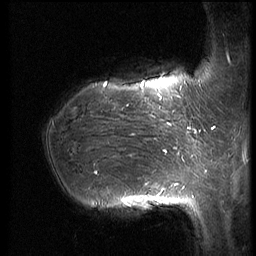
Breast MRI (dynamic contrast-enhanced), one sagittal slice; position 19 of 66 along the scan axis; dynamic contrast-enhanced series, image 2 of 3 at this slice position (ordered by acquisition); 1.5 T; TE 4.2 ms, TR 8.9 ms; 256 × 256 image matrix, field of view 200 × 200 mm. Patient: female, 39 years. Case-level facts recorded for this patient, not image findings: setting: breast cancer imaged before/during neoadjuvant chemotherapy; receptor status: HER2-positive.
Outlined on this slice (semi-automatically segmented with operator editing):
- analysis volume of interest (the breast-tissue region the enhancement analysis was run in; not a lesion): bounding box (x1, y1, x2, y2) in pixels: (41, 75, 188, 218)
- tumour enhancement mask (voxels above the 140 % enhancement threshold inside the analysis volume of interest): (95, 83, 184, 203)